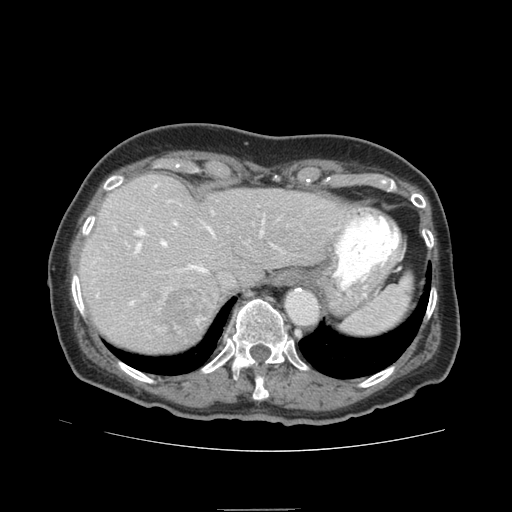
Contrast-enhanced abdominal CT (liver protocol), one axial slice; position 64 of 95 along the scan axis; reconstruction kernel STANDARD; 140 kVp; soft-tissue window (W 400 / L 40 HU); 2.5 mm slice thickness; 512 × 512 image matrix, field of view 360 × 360 mm. From the clinical record (not read from this slice): diagnosis: hepatocellular carcinoma (patient treated with transarterial chemoembolisation; whether this scan precedes or follows treatment is not stated here); TNM stage (as recorded): Stage-IVA; Child-Pugh class: B; tumour differentiation: moderately differentiated; tumour nodularity: uninodular.
Annotated regions visible in this slice (semi-automatic segmentation, software-assisted and operator-edited):
- liver parenchyma outside the tumour (the mass and vessels are separate outlines, so this box may not span the whole liver): bounding box (x1, y1, x2, y2) in pixels: (80, 174, 348, 352)
- mass: (141, 283, 206, 339)
- liver vessels: (97, 185, 272, 306)